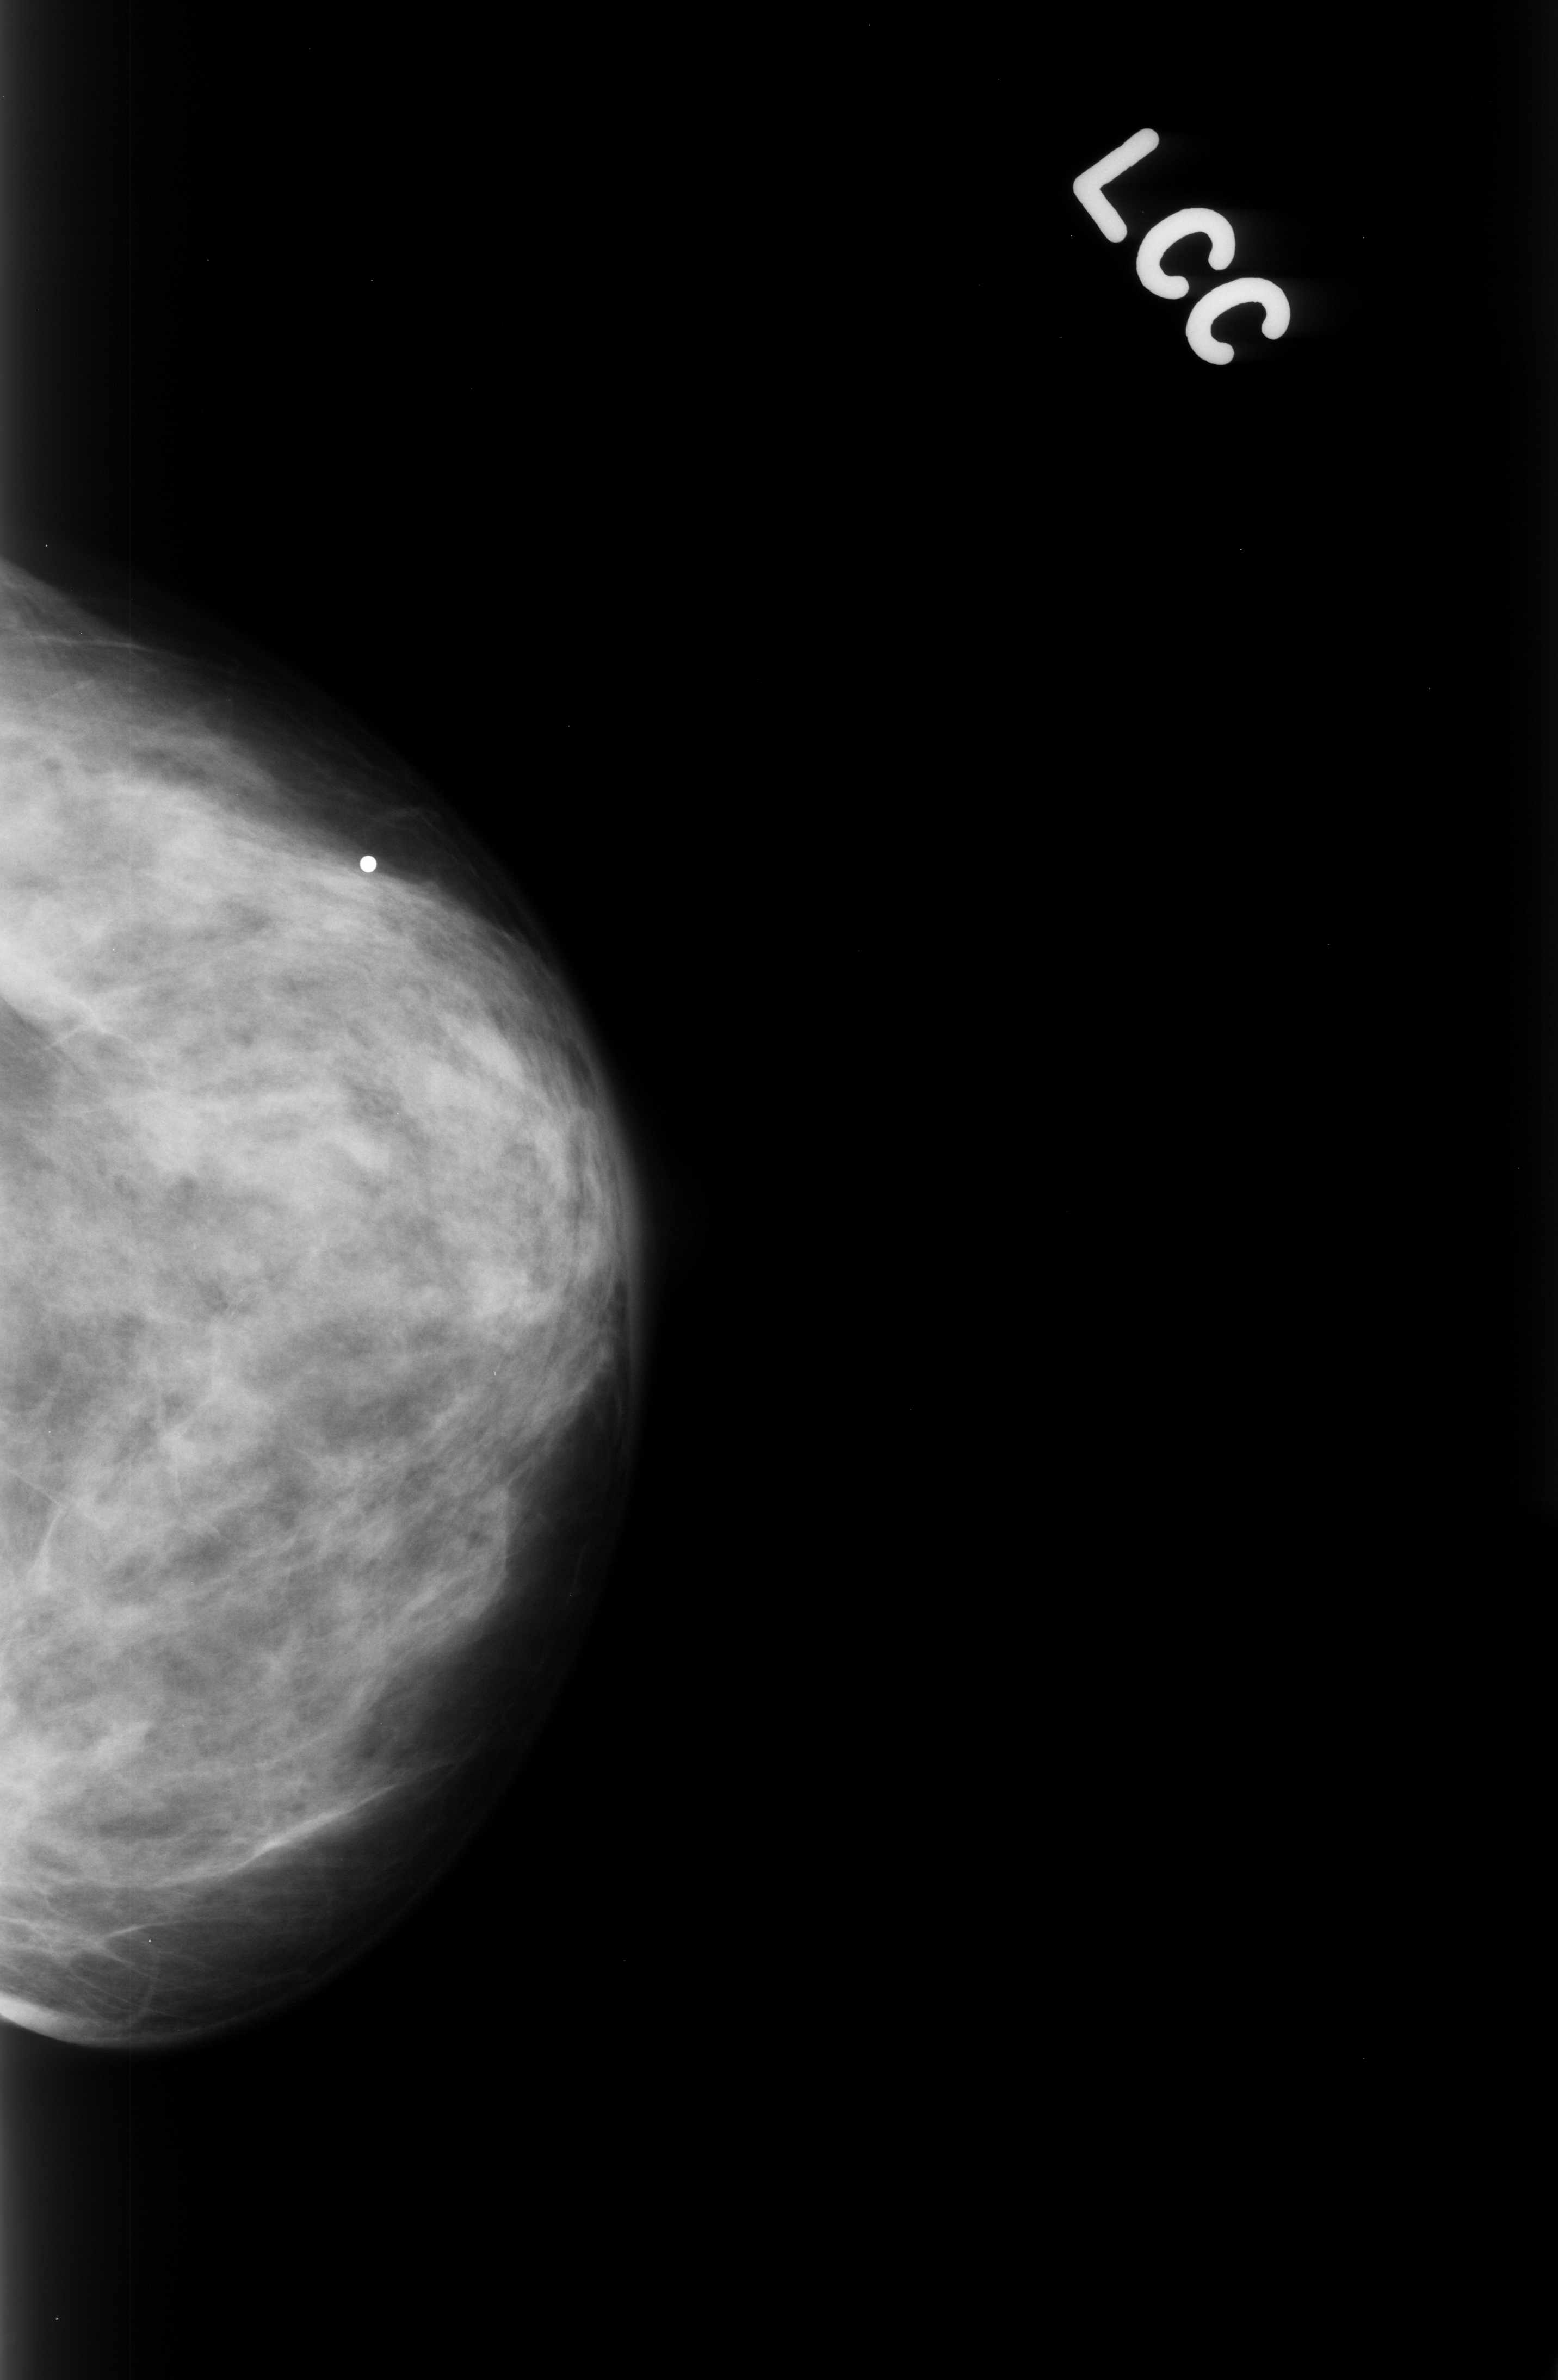
Mammogram (digitized film). Left breast. CC view. BI-RADS breast density category 3 (scale 1–4). 1558 × 2380 image matrix.
Expert-marked regions of interest on this image (one box per marked abnormality):
- mass, shape oval, margins circumscribed; BI-RADS assessment category 3; pathology (as recorded): benign: box from (x=15, y=922) to (x=160, y=1070) px